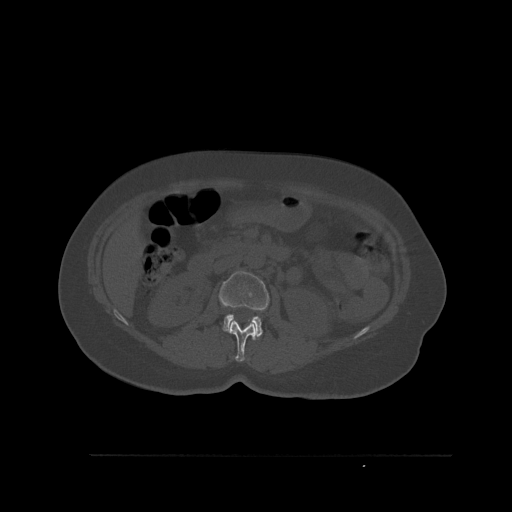
CT including the spine, one axial slice; slice 255 of 527 in the series (ordered by position); bone window (W 1800 / L 400 HU); 512 × 512 image matrix. Patient: female, 73 years. Case-level facts recorded for this patient, not image findings: primary cancer: breast.
Annotated regions visible in this slice (semi-automatic segmentation, software-assisted and operator-edited):
- L1 vertebra: bounding box [x1, y1, x2, y2] px = [229, 320, 257, 362]
- L2 vertebra: [219, 271, 269, 338]